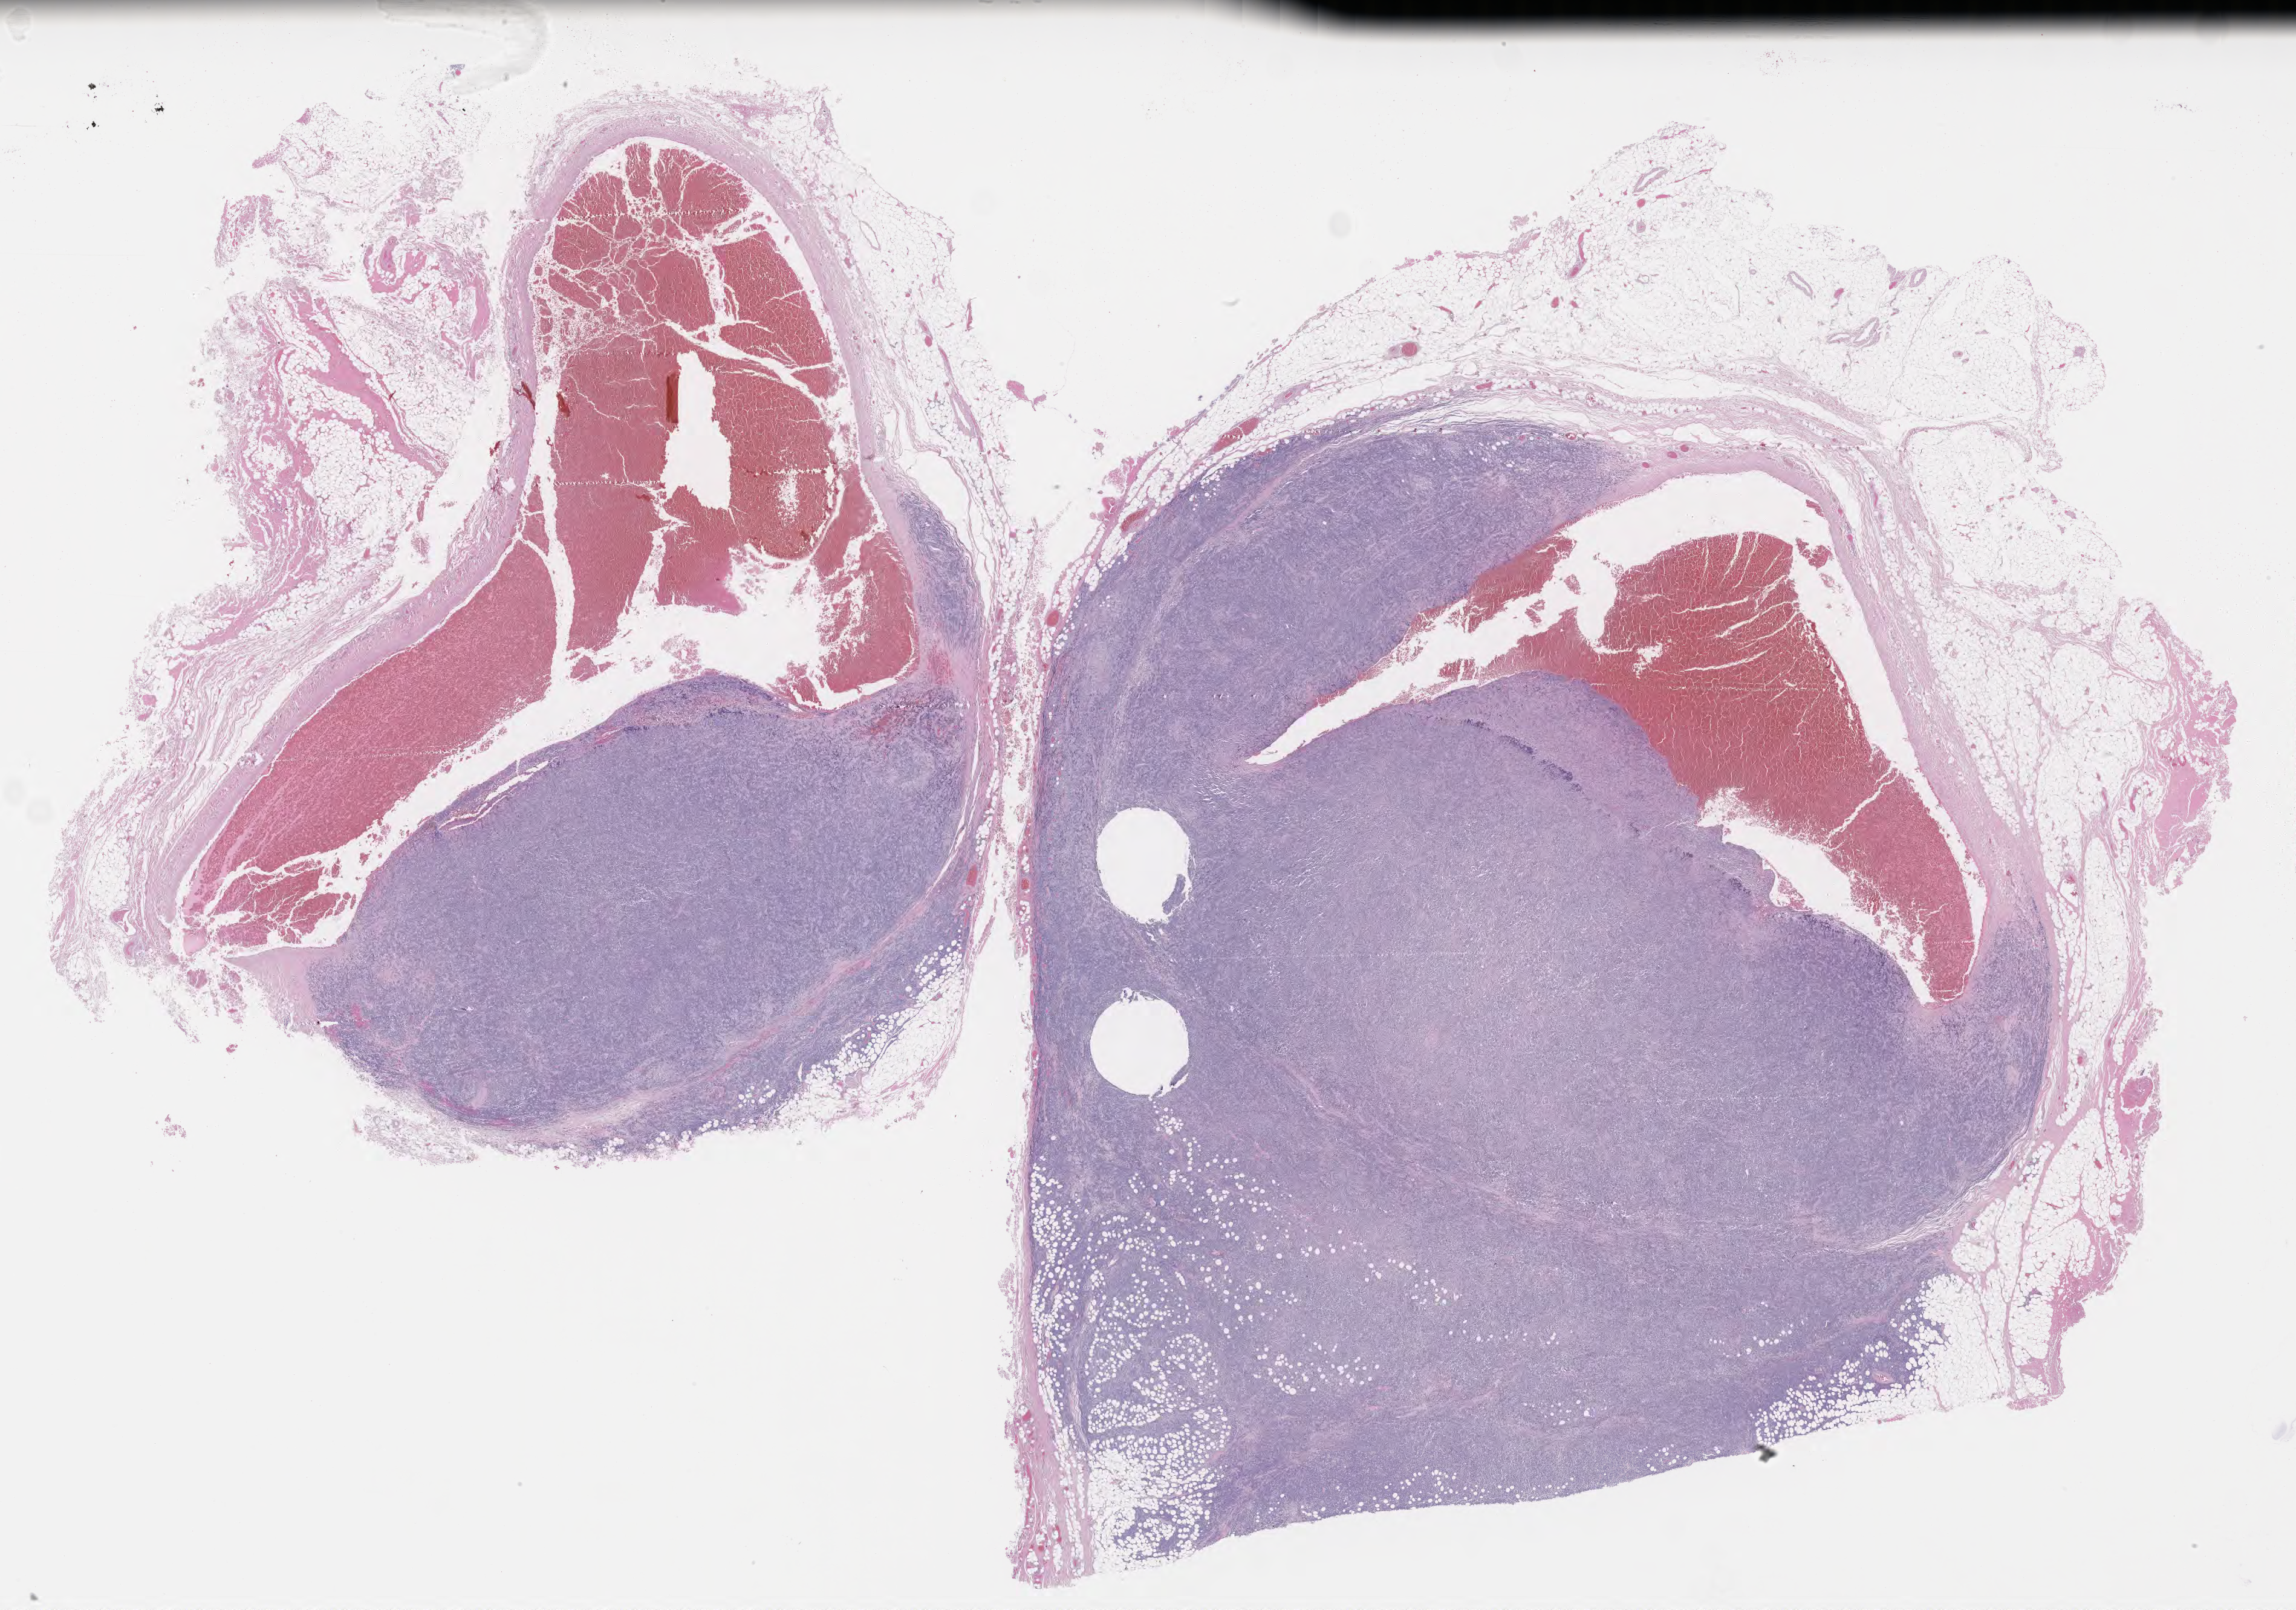
Whole-slide image, H&E stain, a low-resolution overview of the entire scanned area, about 30.7 x 21.5 mm, specimen: tumor tissue, site: soft tissue of head and neck. Patient male; 67 years old.
Histologic diagnosis: Burkitt lymphoma, NOS.